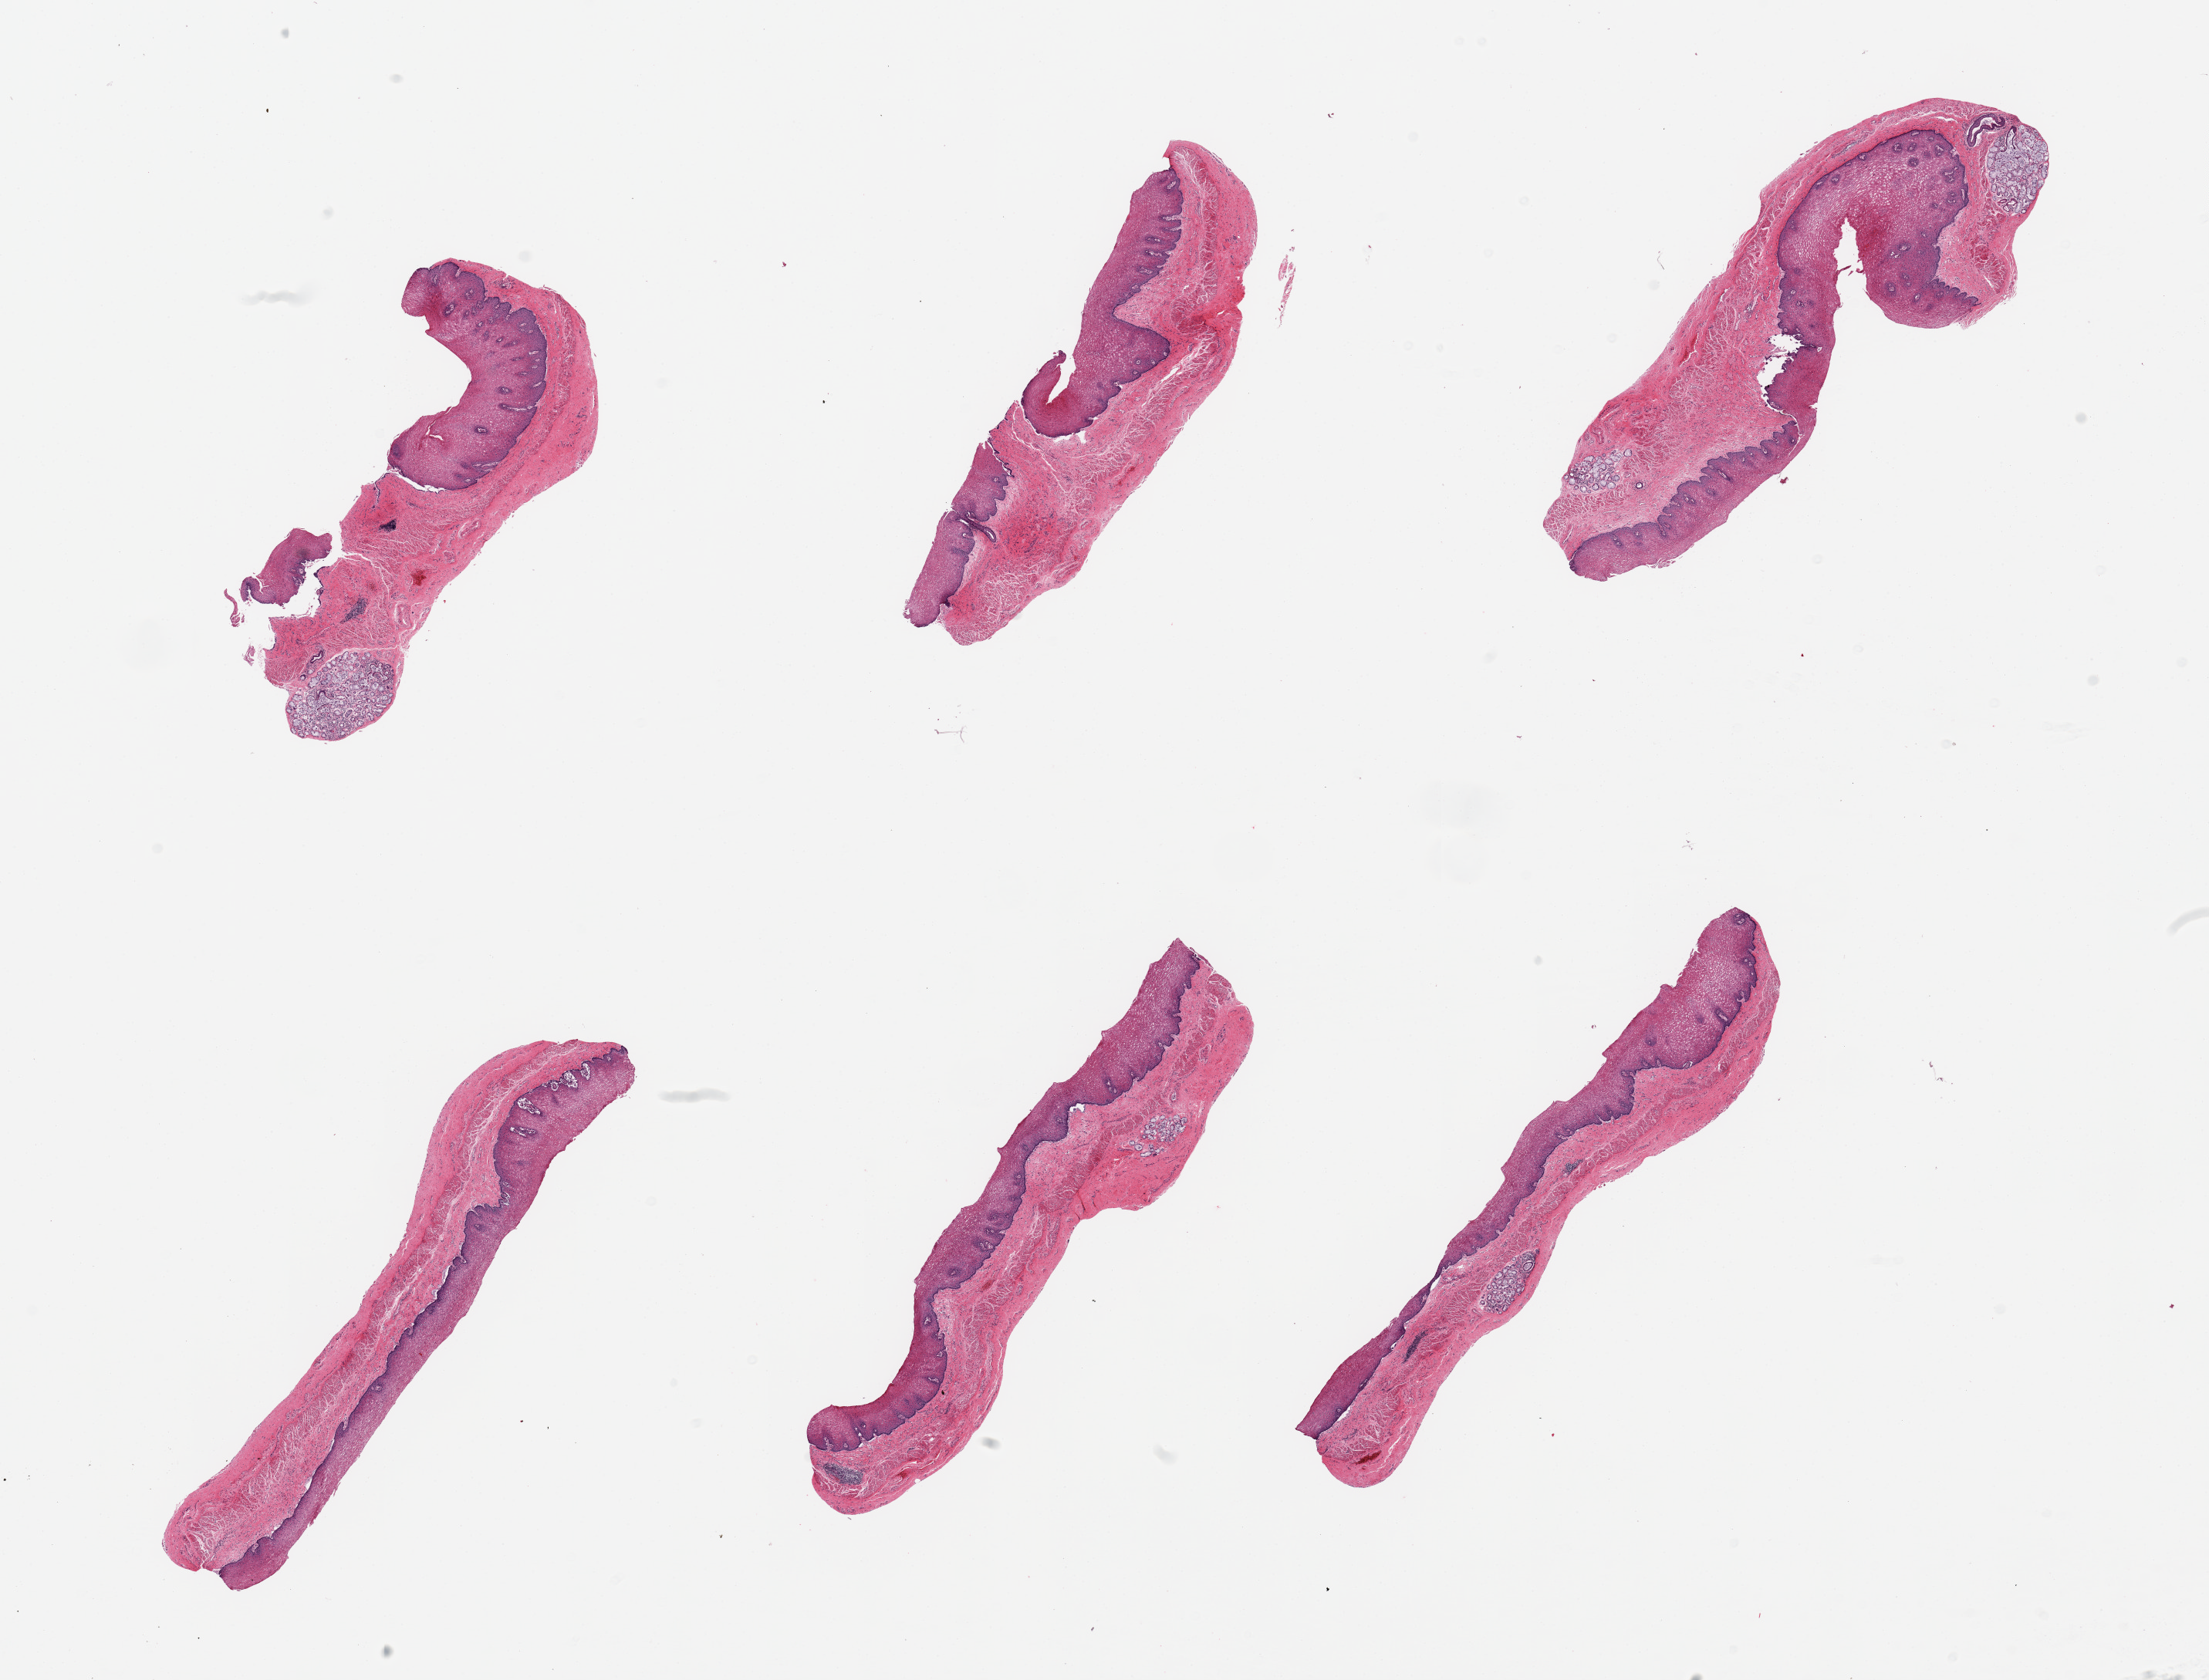
Whole-slide image, haematoxylin and eosin stain, brightfield, a low-resolution overview of the entire scanned area, about 22.6 x 17.2 mm (slide scanned at 20x); PAXgene-fixed, paraffin-embedded tissue; section of esophageal mucous membrane (target tissue); tissue donor sample. Male donor.
Review note (as recorded): 6 pieces, squmaous mucoa up to ~0.5mm, ~50% thickness; Submucosal mucus glands prominent.